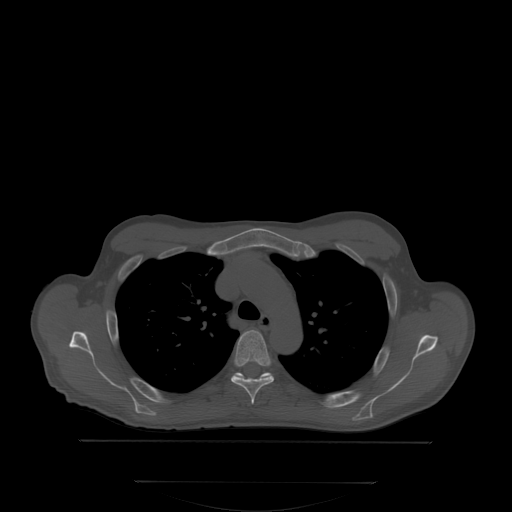
CT including the spine, one axial slice. Slice 256 of 350 in the series (ordered by position). Bone window (W 1800 / L 400 HU). 2.5 mm slice thickness. 512 × 512 image matrix, field of view 500 × 500 mm. Male patient, age 58 years. From the clinical record (not read from this slice): primary cancer: prostate.
Outlined on this slice (semi-automatic segmentation, software-assisted and operator-edited):
- T4 vertebra: bounding box <231,330,273,404> (left, top, right, bottom; pixels)
- T5 vertebra: <233,372,272,379>